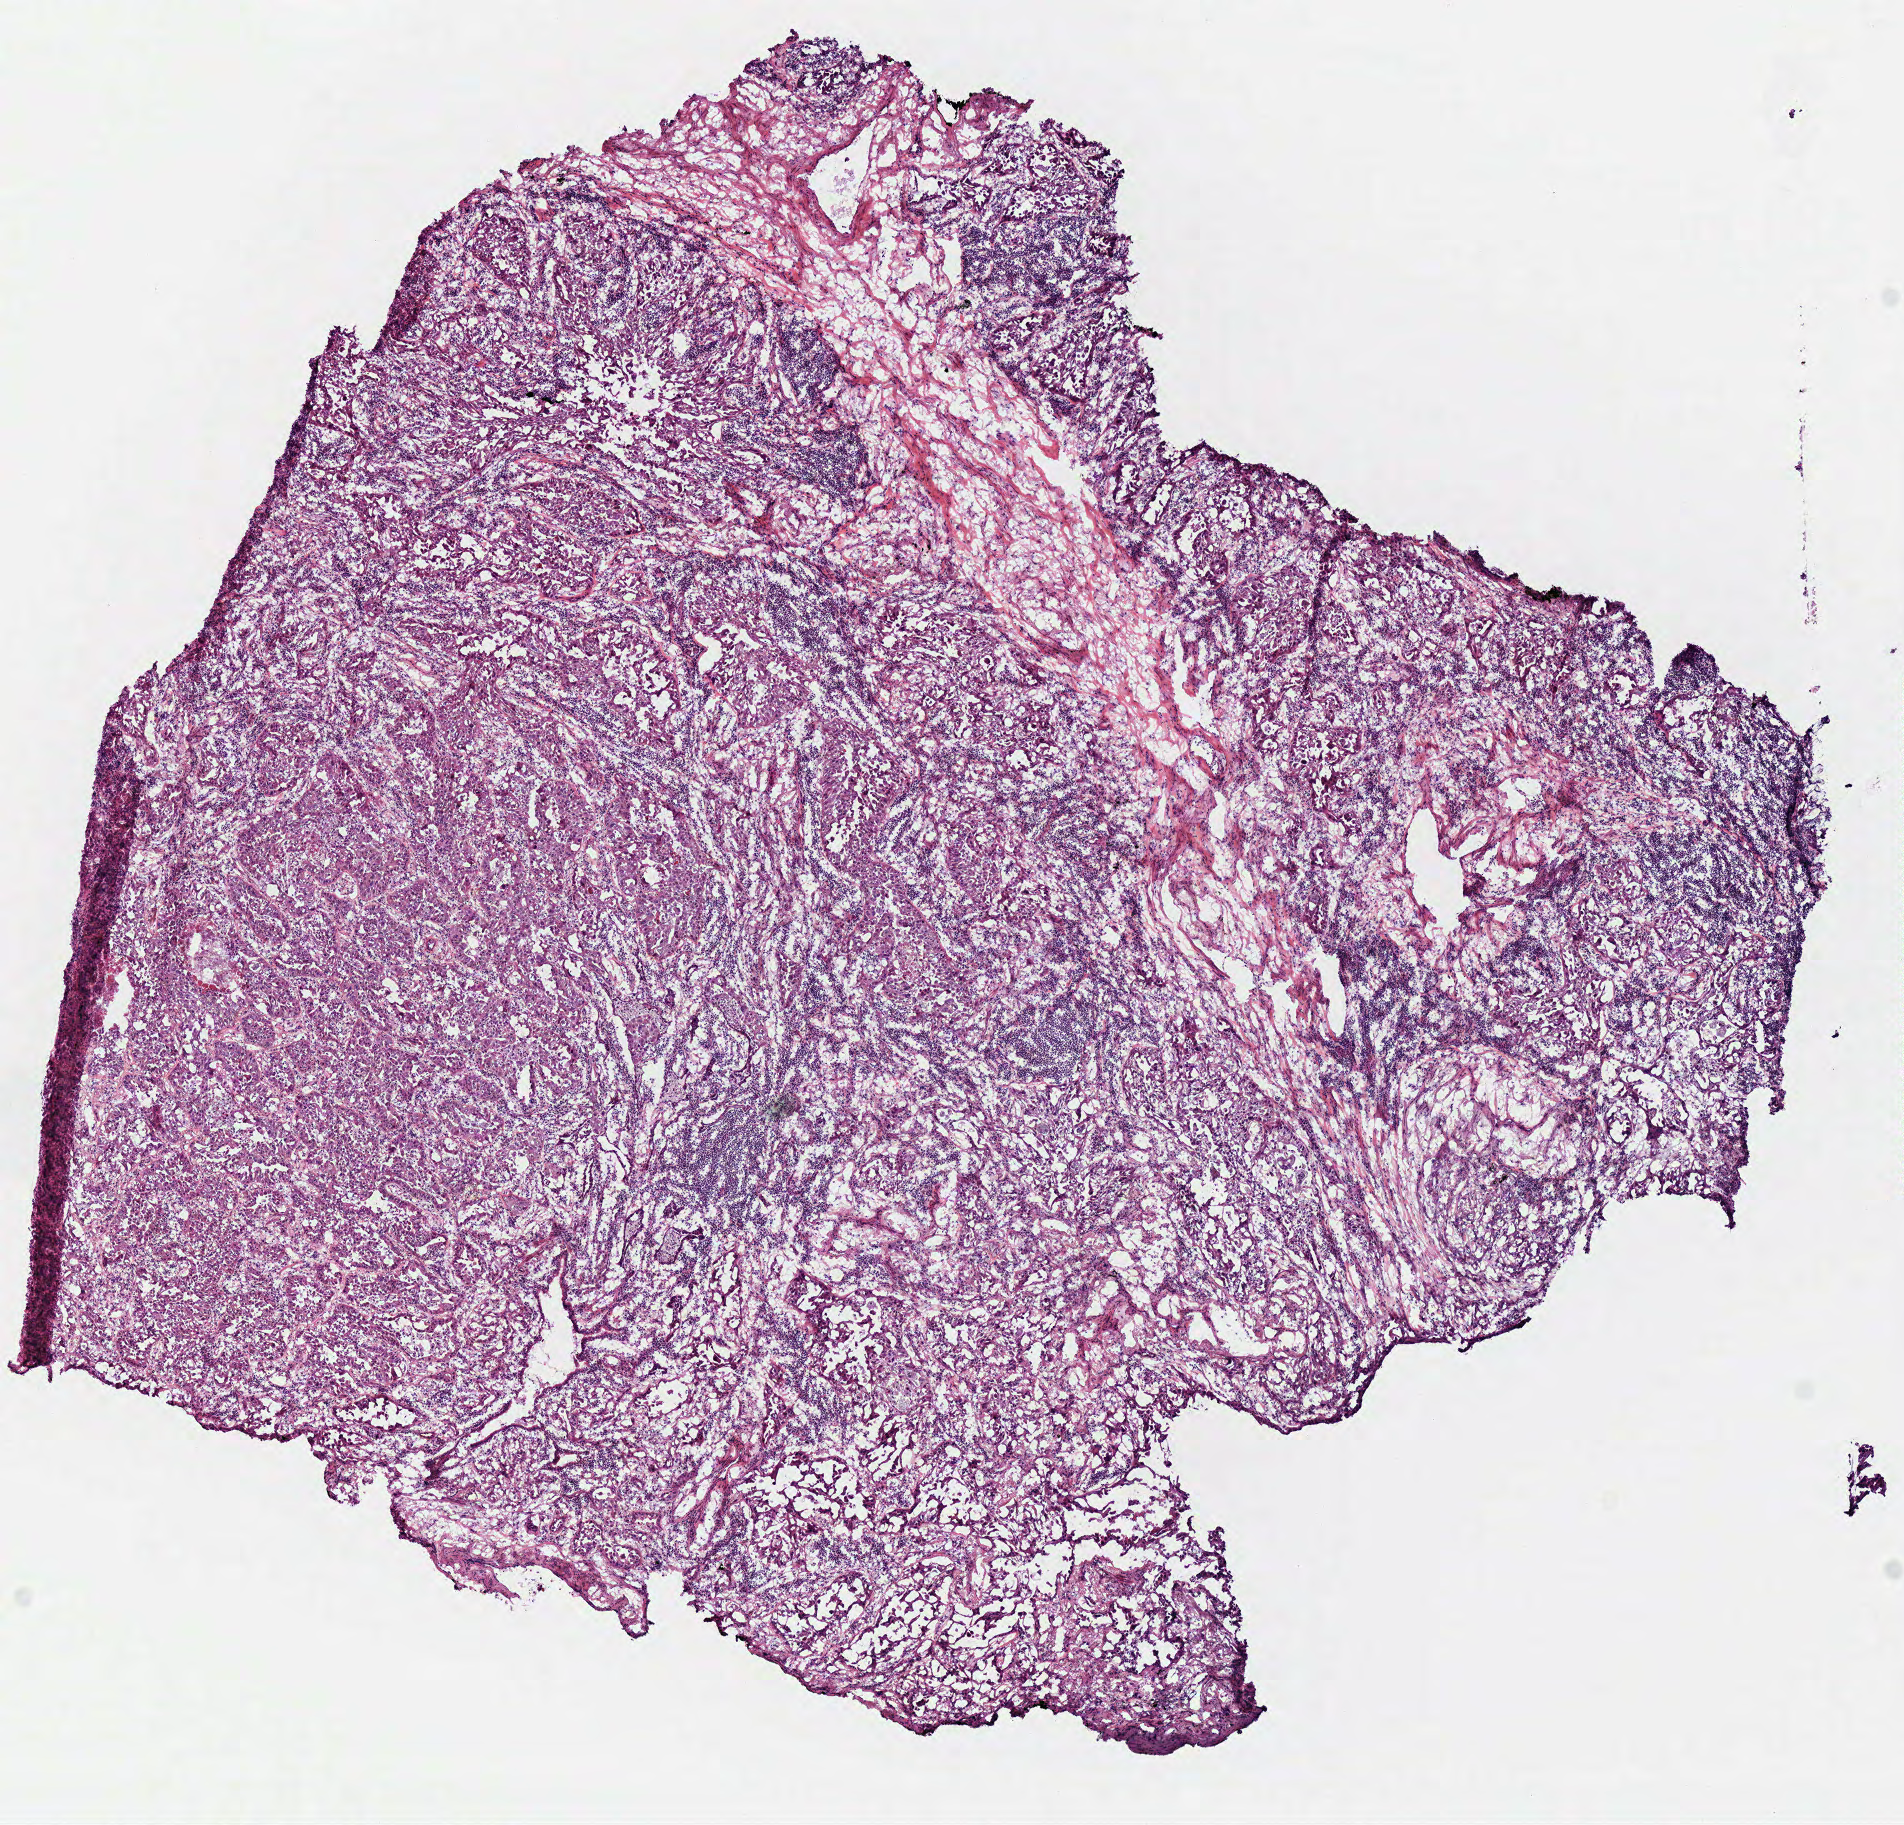
H&E-stained whole-slide image — shown as a low-resolution overview of the whole scanned area (about 7.5 x 7.2 mm, acquisition: 40x scan). Frozen section from the top of the tissue portion. Sample: primary tumour, lung. Patient: male, age at initial diagnosis 71 years. Slide review estimates, as recorded: tumour cells 85%, tumour nuclei 60%, normal cells 0%, stromal cells 15%, necrosis 0%. Infiltration values recorded for this section: lymphocyte infiltration 30%, monocyte infiltration 0%, neutrophil infiltration 0%.
- AJCC pathologic stage: IIA
- histologic diagnosis: Adenocarcinoma, NOS (upper lobe, lung)
- laterality: left